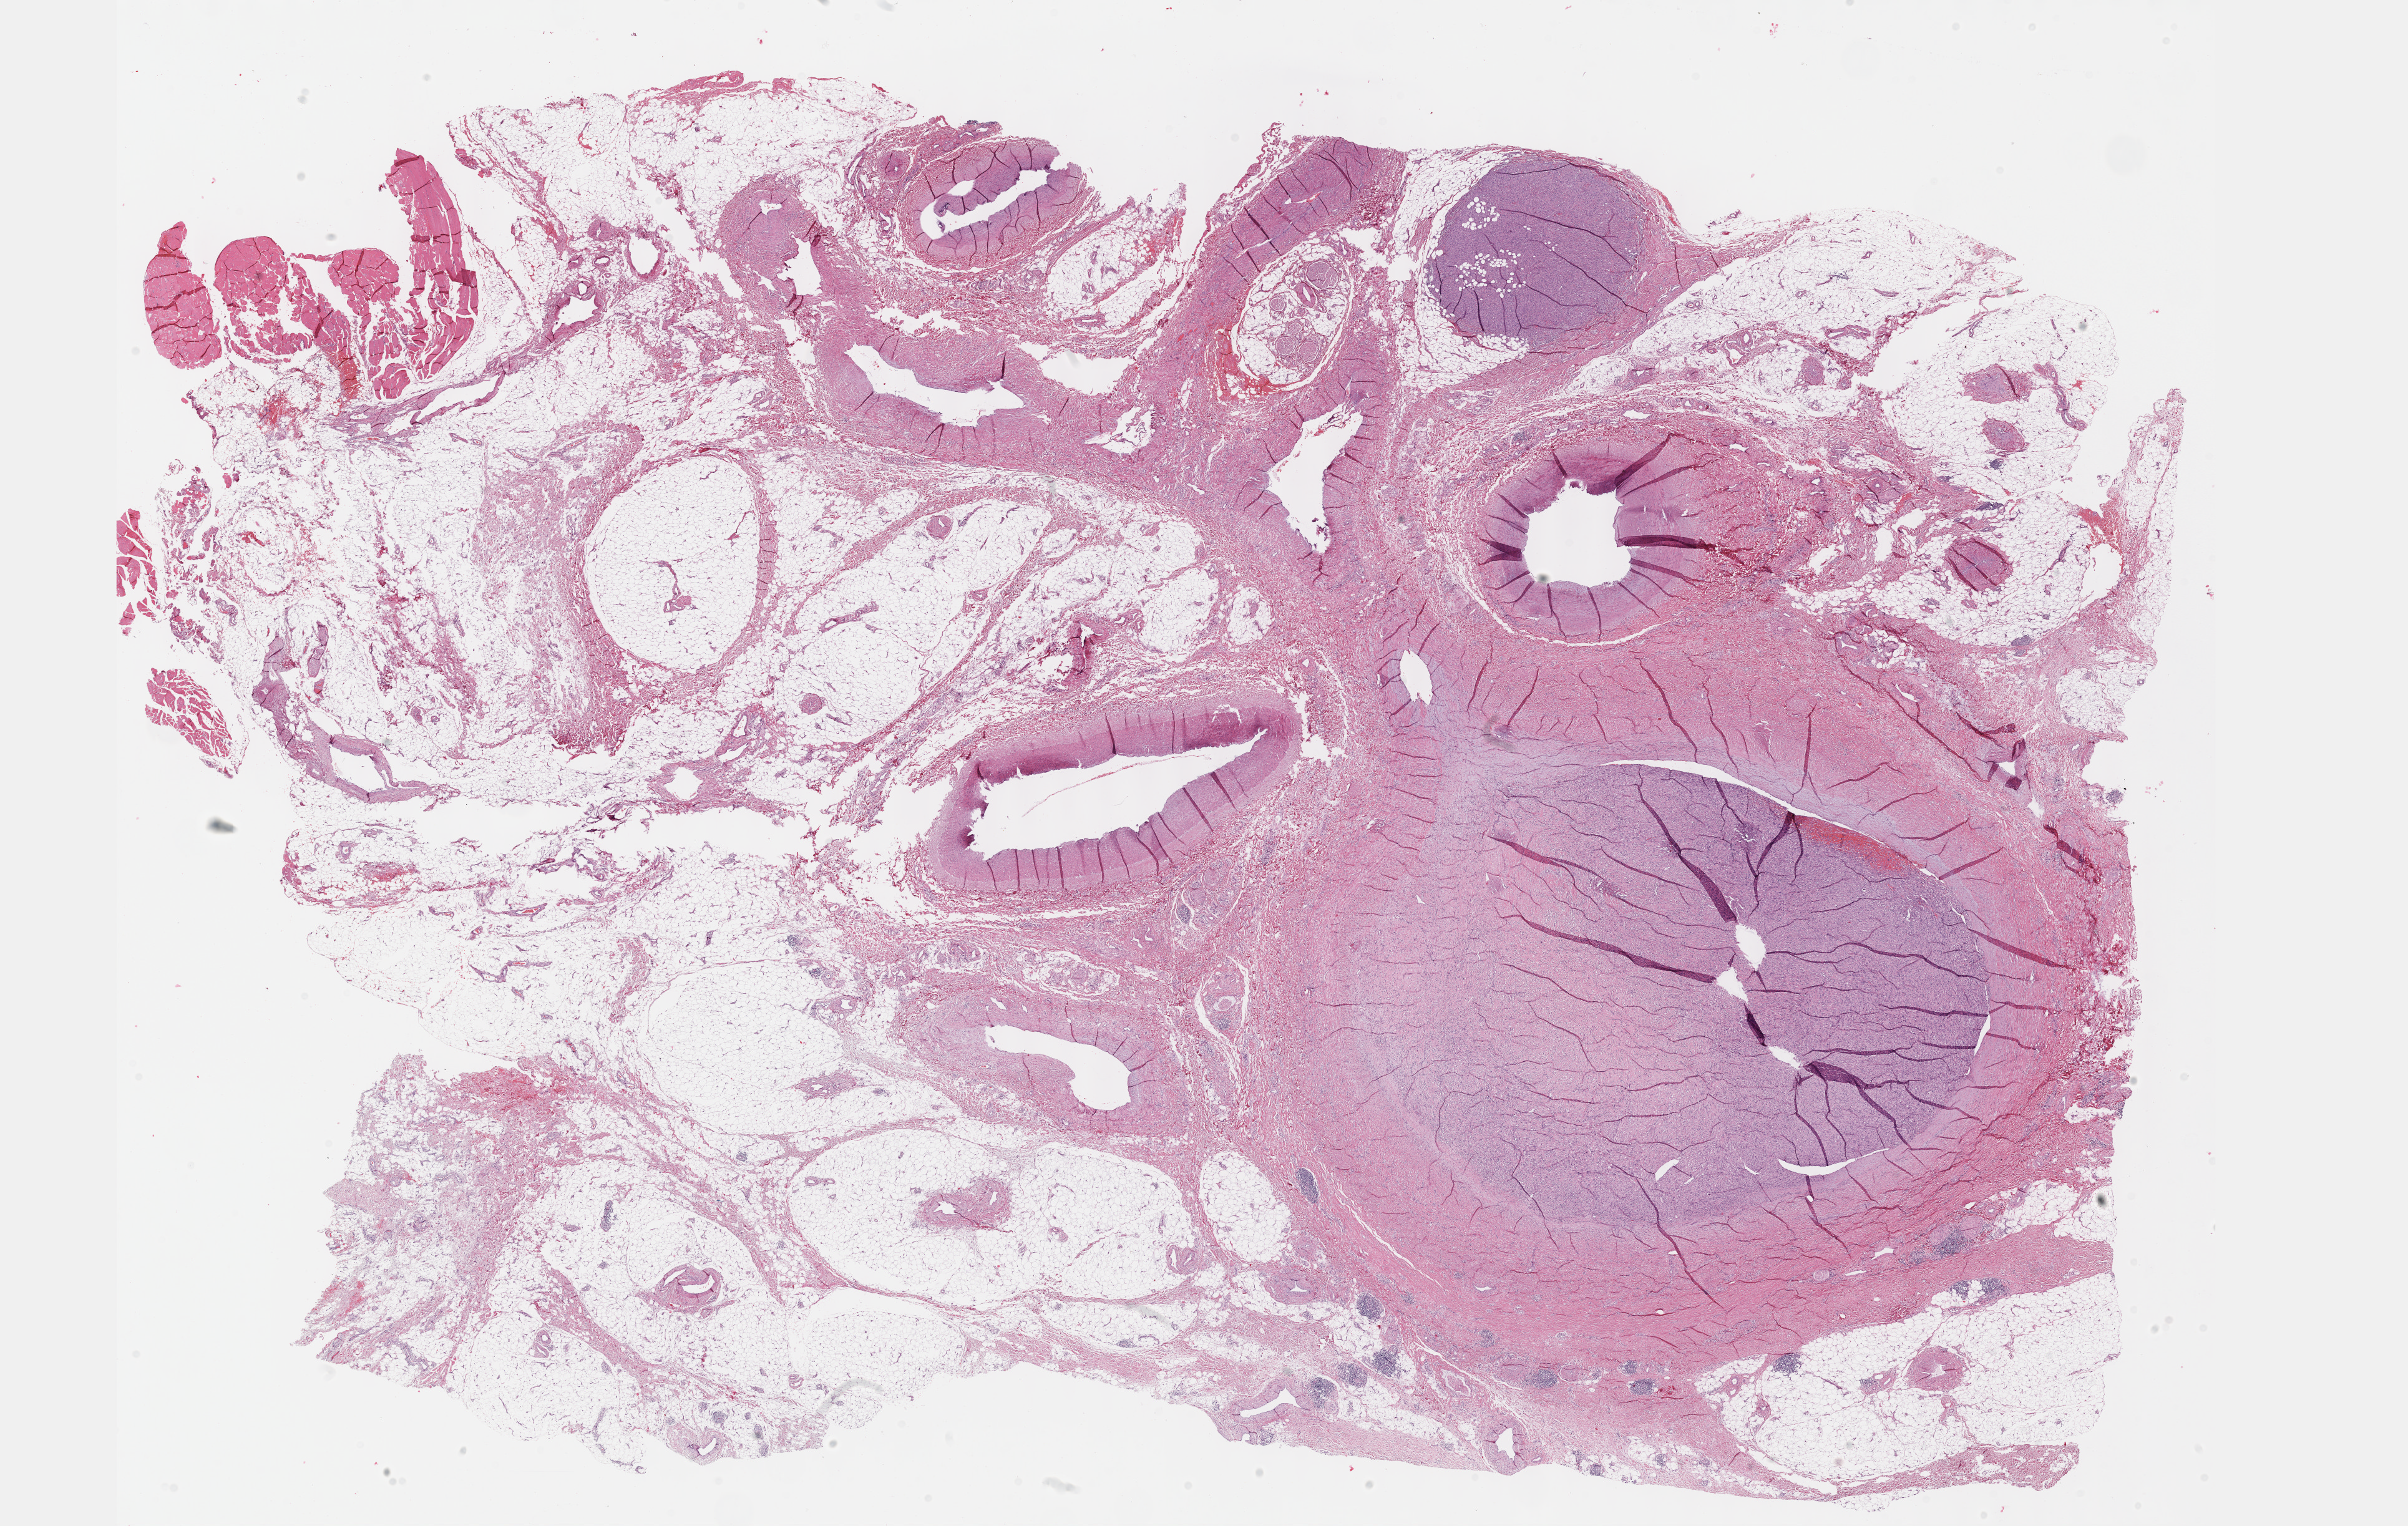
Digitized H&E-stained tissue section (whole slide), low-resolution overview of the scanned area, about 31.2 x 19.8 mm, formalin-fixed paraffin-embedded (FFPE) diagnostic section, sample: primary tumour, connective, subcutaneous and other soft tissues. Female patient; age at initial diagnosis 53 years.
Pathologic diagnosis: Leiomyosarcoma, NOS.